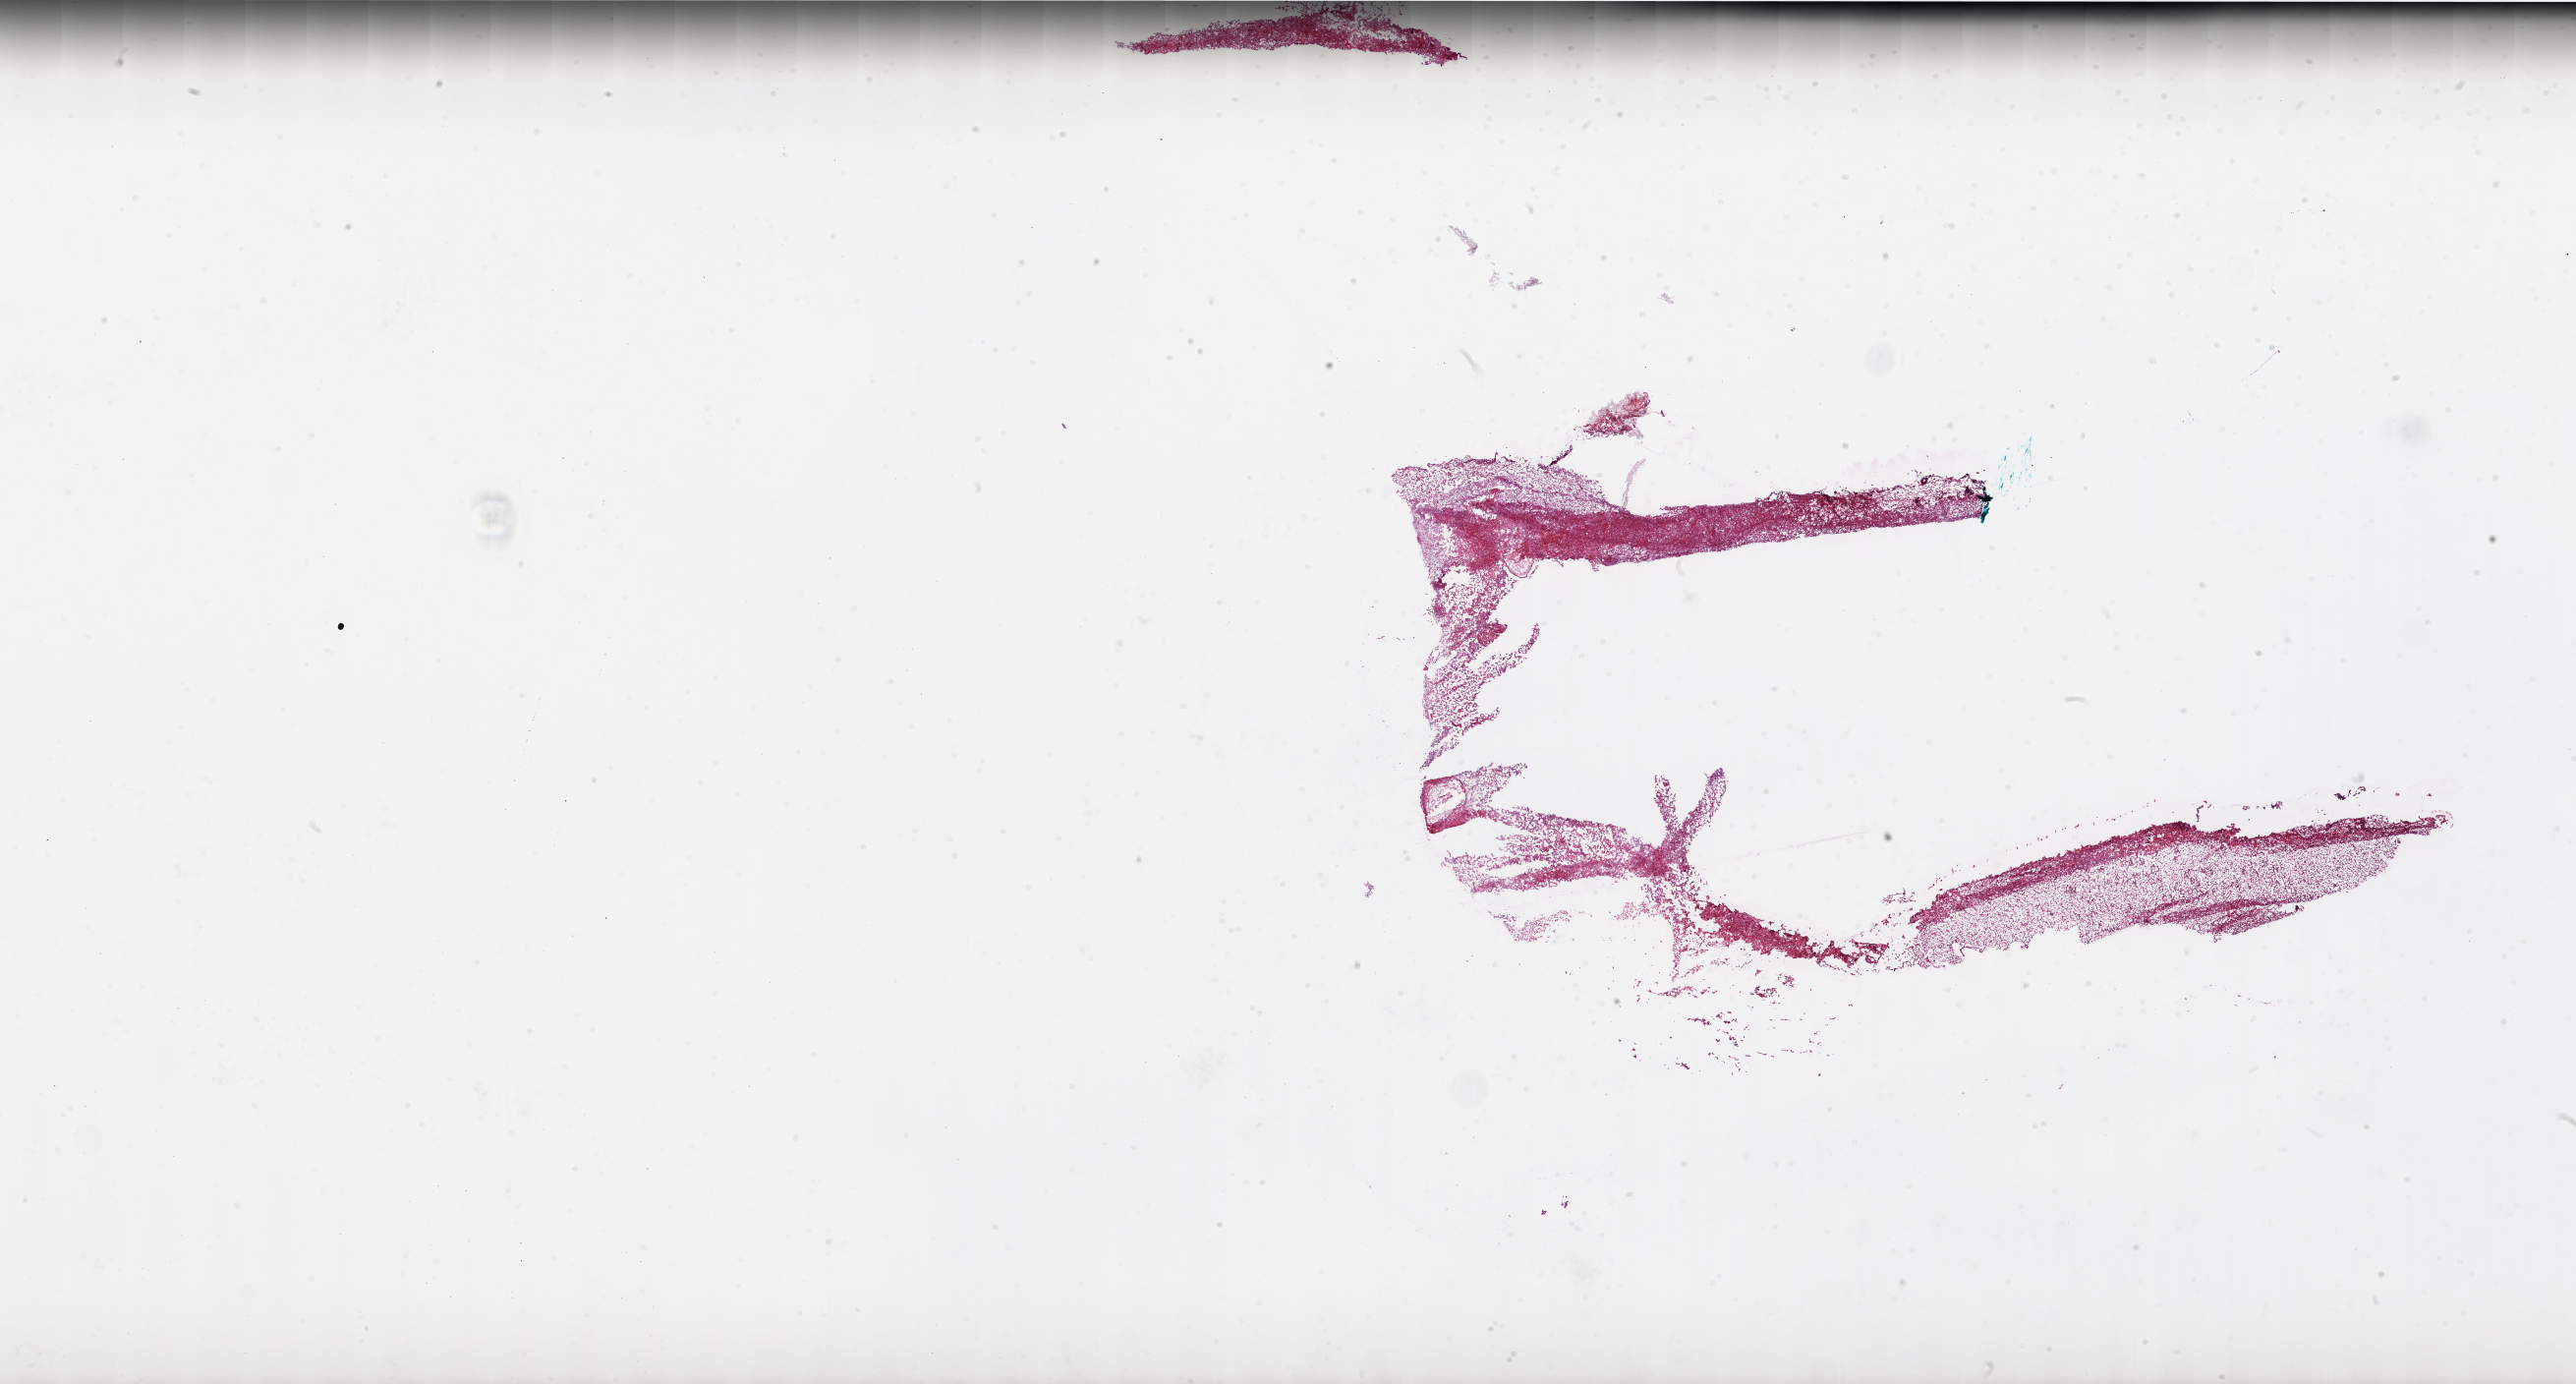
Digitized H&E-stained tissue section (whole slide), a low-resolution overview of the entire scanned area, about 42.0 x 22.5 mm (acquisition: 20x scan), frozen section from the bottom of the tissue portion, primary tumour sample from the brain. Female patient; age at initial diagnosis 50 years. Composition of this section per pathologist review: tumour cells 70%, tumour nuclei 100%, normal cells 0%, stromal cells 0%, necrosis 30%. Inflammatory infiltration, as recorded: lymphocyte infiltration 0%.
Diagnosis: Glioblastoma.